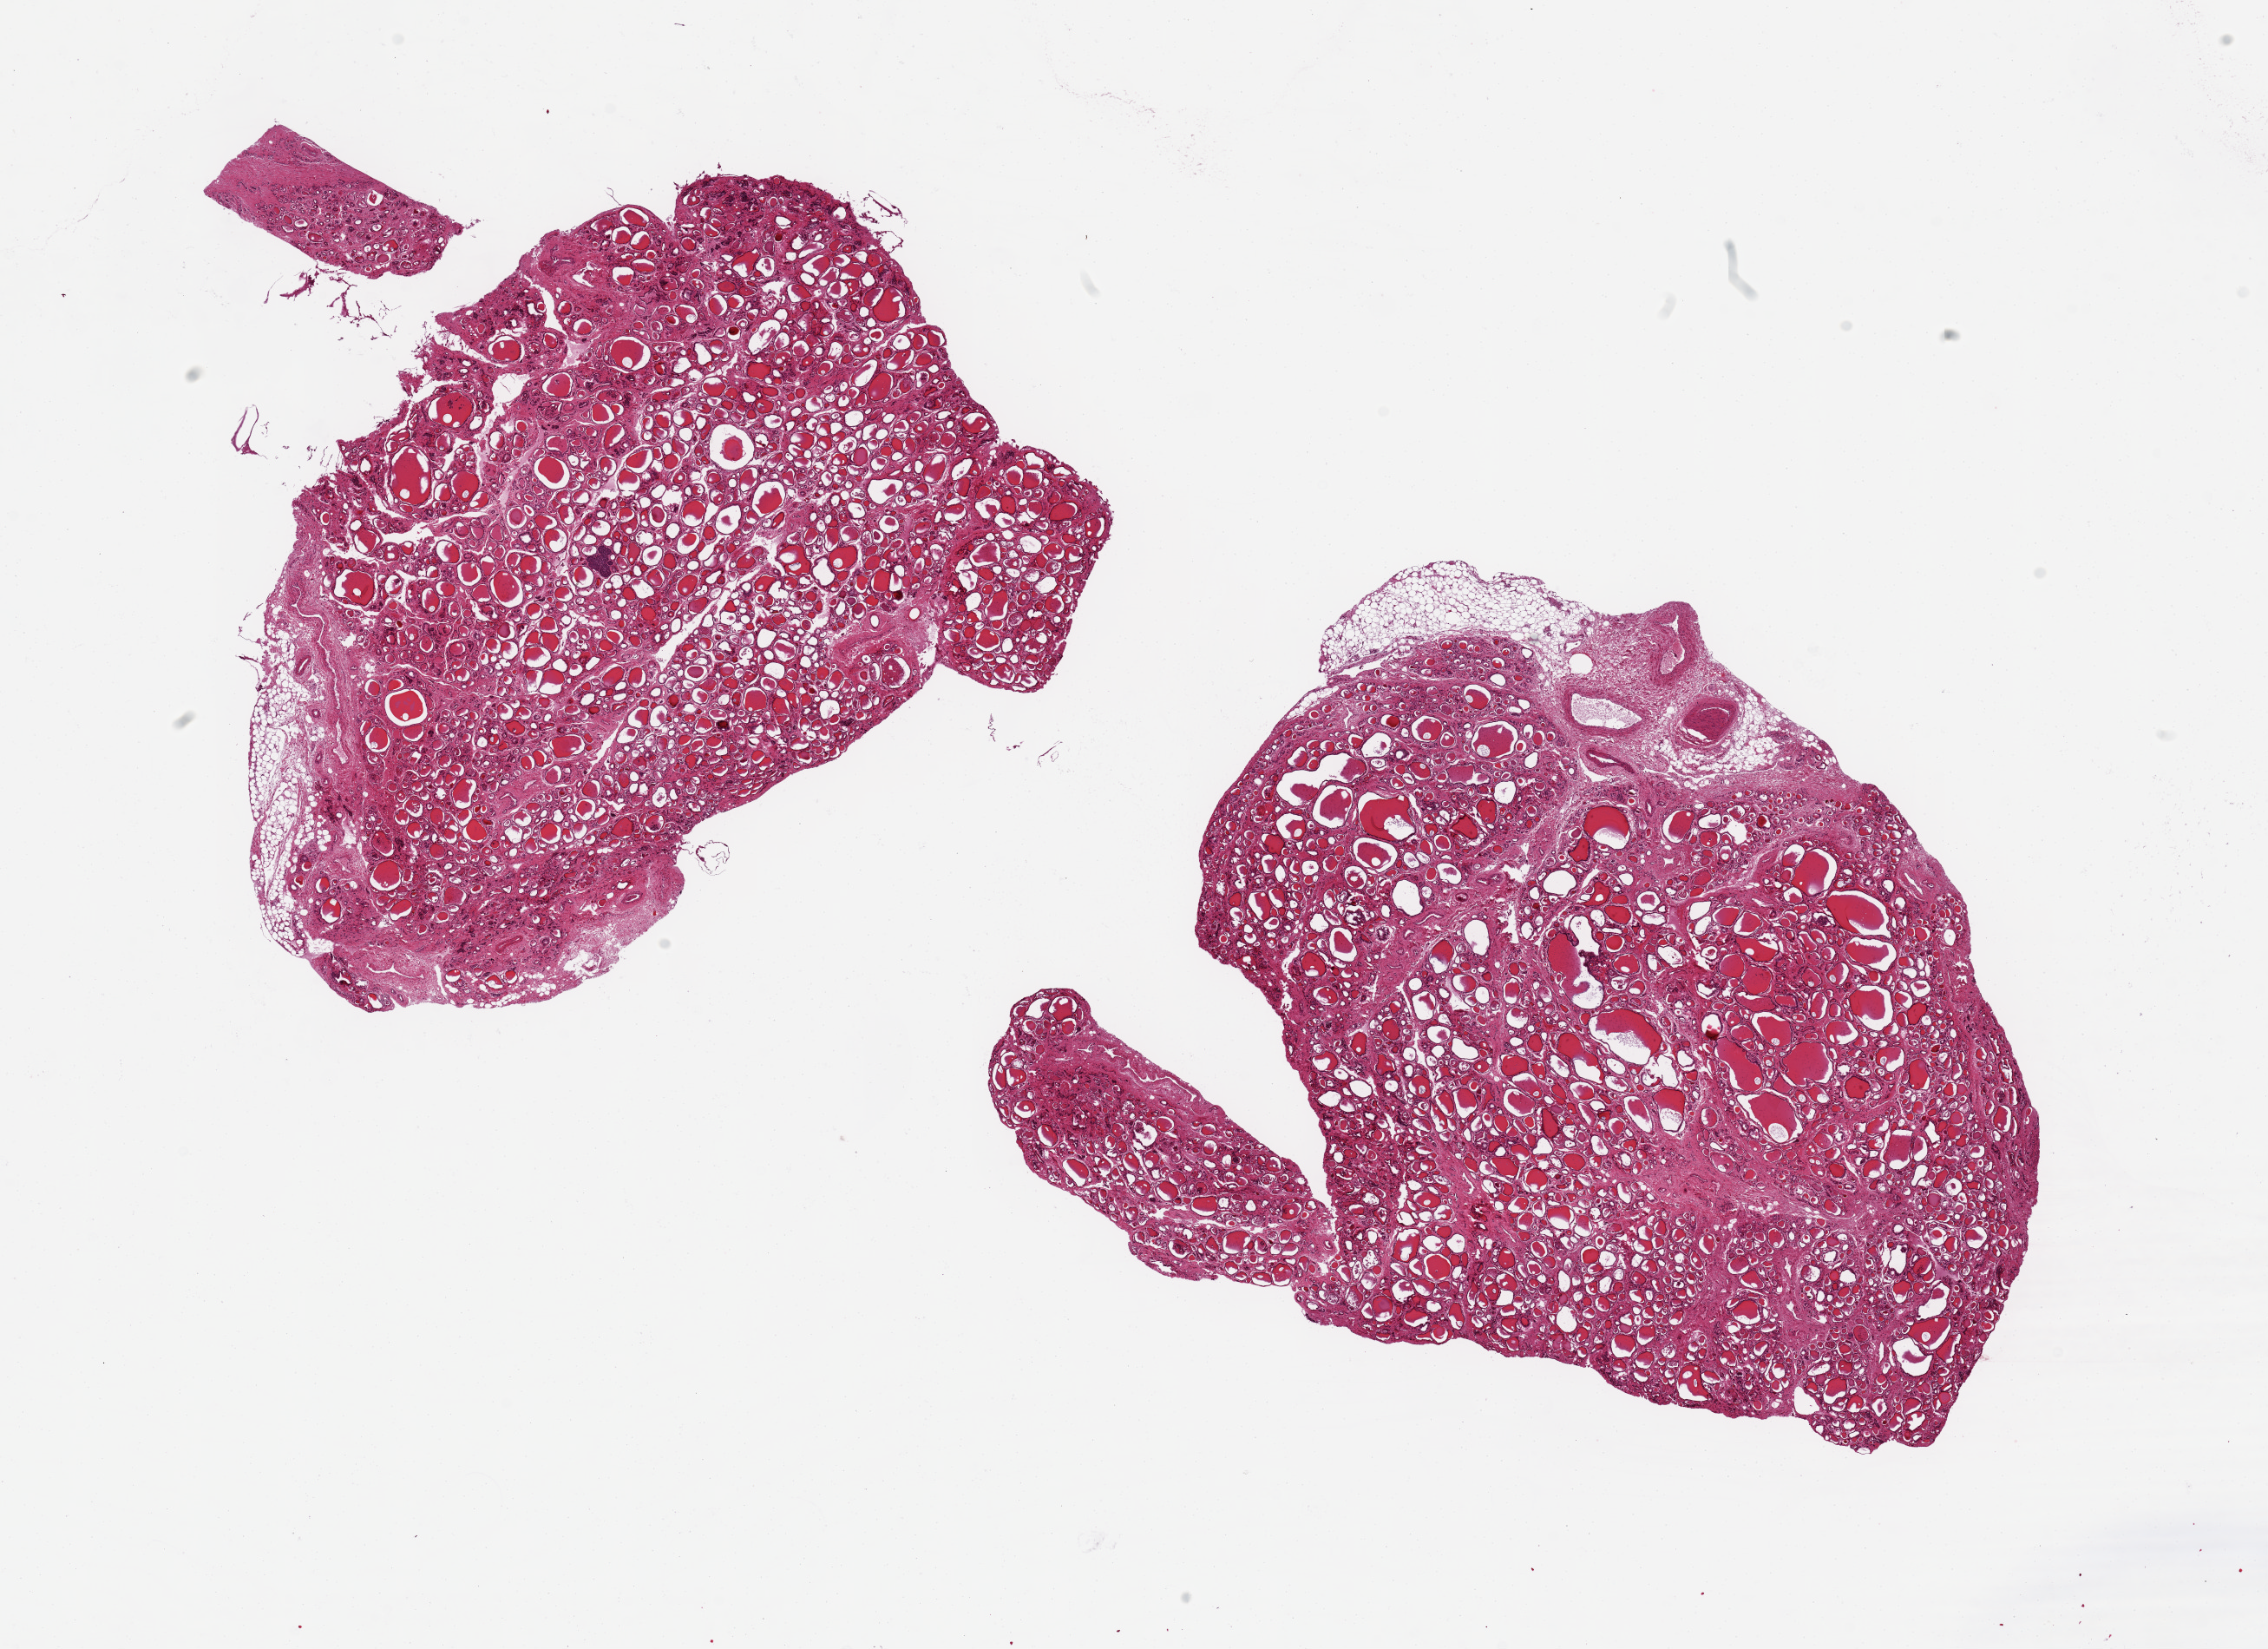
Whole-slide image, hematoxylin and eosin (H&E) stain, brightfield, a low-resolution overview of the entire scanned area, about 20.7 x 15.0 mm (acquisition: 20x scan). PAXgene-fixed paraffin-embedded (PFPE) section. Section of thyroid (target tissue). Tissue donor sample. Donor: male.
Pathologist's review note for this sample: 2 aliquots. Patchy regressive changes.